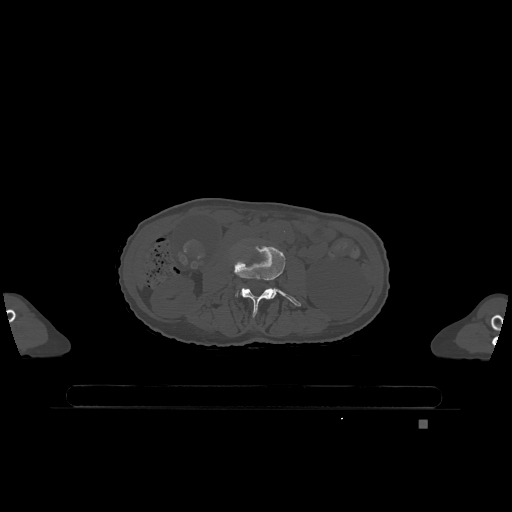
CT including the spine, one axial slice. Slice 349 of 1317 in the series (ordered by position). Bone window (W 1800 / L 400 HU). 0.5 mm slice thickness. 512 × 512 image matrix, field of view 500 × 500 mm. Patient: female, 74 years. Case-level facts recorded for this patient, not image findings: primary cancer: lung; vertebrae with lytic lesions (as recorded): T1, T4, T5, T6, L4, L5.
Annotated regions visible in this slice (semi-automatic segmentation, software-assisted and operator-edited):
- L3 vertebra: bounding box <234,245,301,317> (left, top, right, bottom; pixels)
- L4 vertebra: <236,293,238,297>